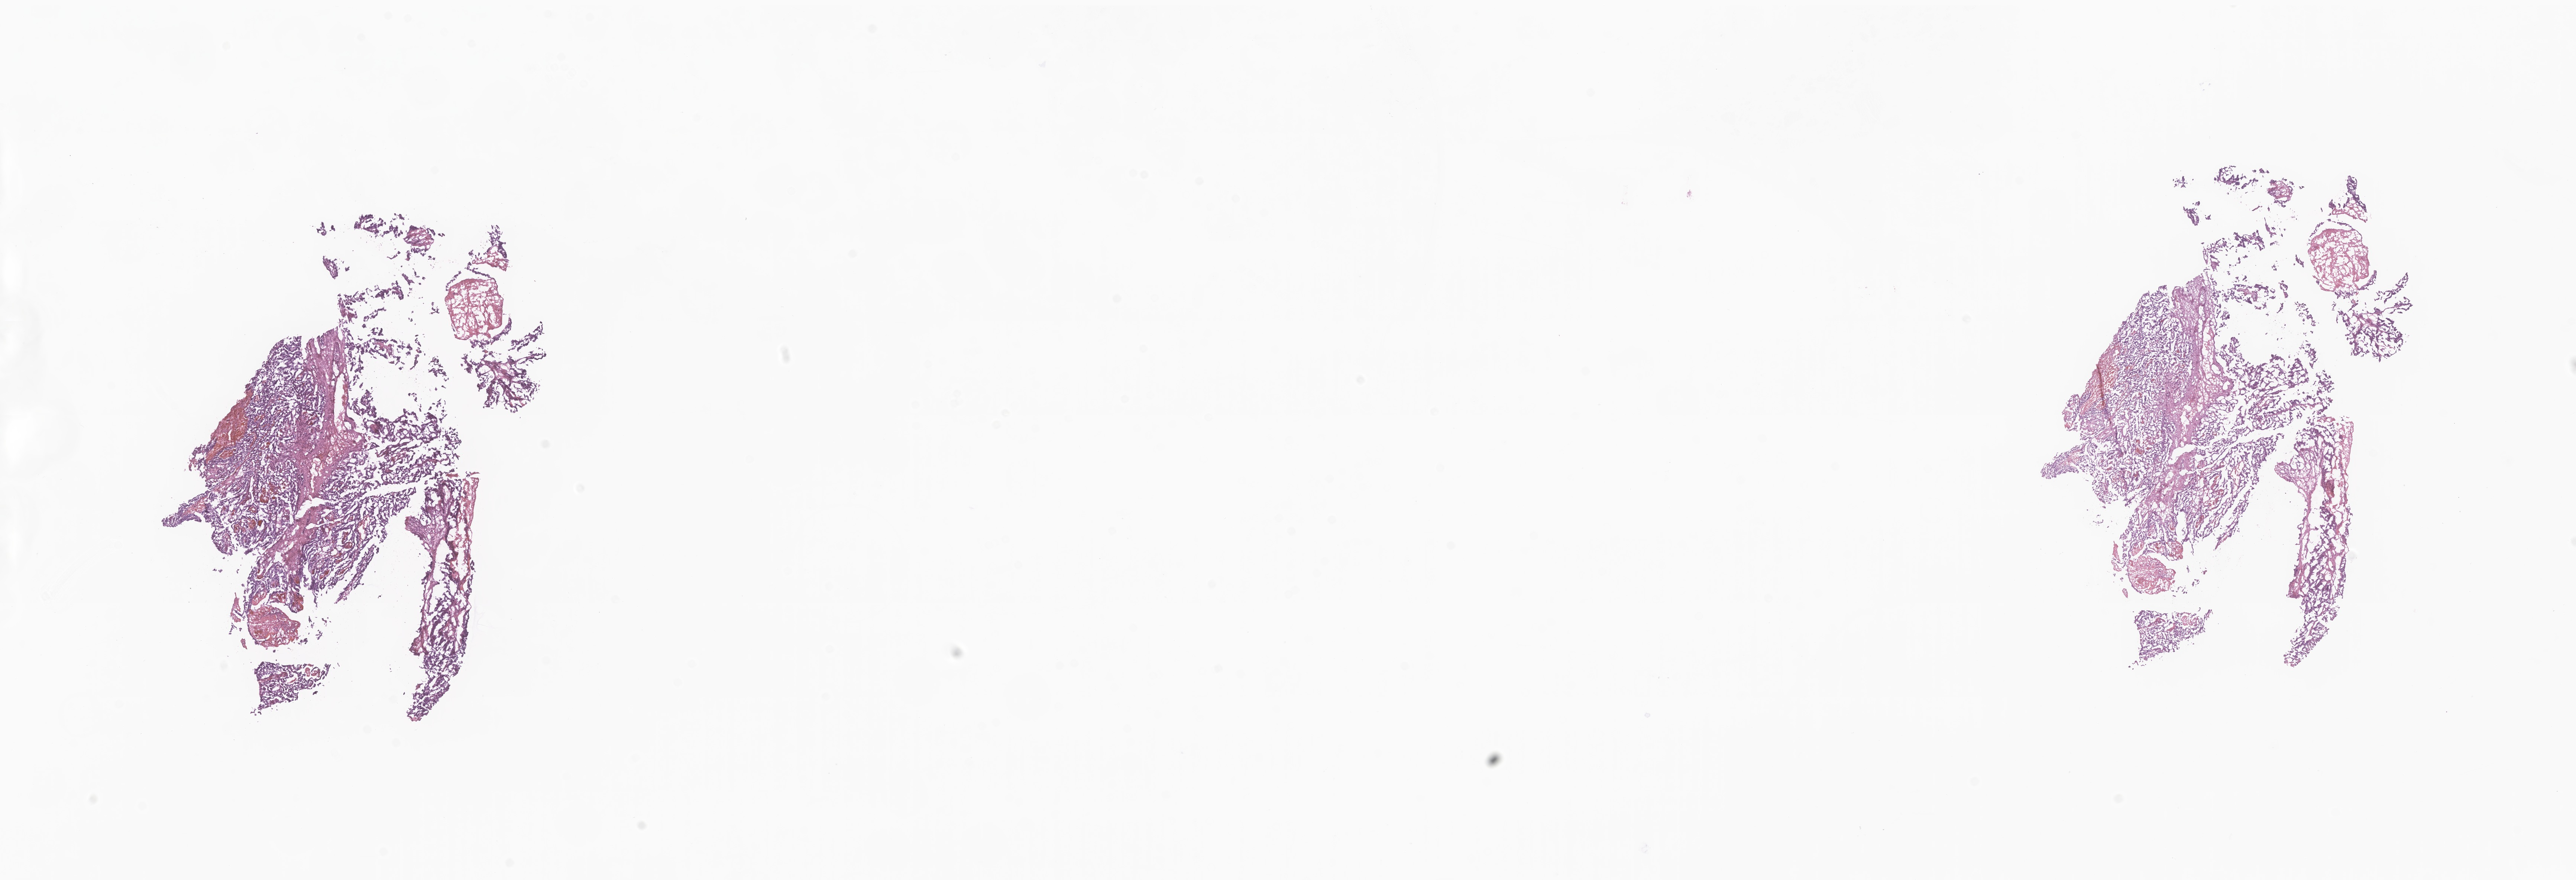
Whole-slide image, haematoxylin and eosin stain of tumor tissue from the cerebral ventricle, whole scanned area (about 29.2 x 10.0 mm) shown as a low-resolution overview; frozen section (OCT-embedded). Patient male; age 131 days.
Diagnosis: Choroid plexus papilloma, NOS.